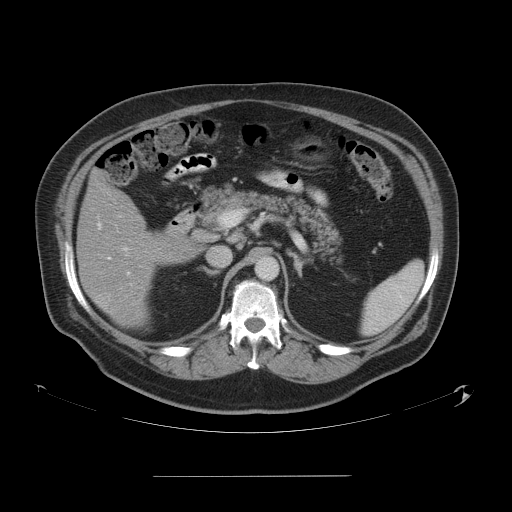
Contrast-enhanced abdominal CT, one axial slice; slice 29 of 58 in the series (ordered by position); 120 kVp; intravenous contrast given; soft-tissue window (W 400 / L 40 HU); 5 mm slice thickness; 512 × 512 image matrix, field of view 480 × 480 mm. Male patient, age 63 years. From the clinical record (not read from this slice): diagnosis: colorectal cancer liver metastases, imaged before liver resection; multiple liver metastases: no; largest metastasis: 4.2 cm; disease in both lobes: no.
Outlined on this slice (outlined manually by an expert reader):
- hepatic veins: box from (x=126, y=250) to (x=130, y=275) px
- liver: (x=78, y=172)–(x=195, y=327)
- planned liver remnant (the part of the liver to remain after resection): (x=78, y=179)–(x=195, y=327)
- portal vein (with intrahepatic branches): (x=98, y=223)–(x=131, y=285)